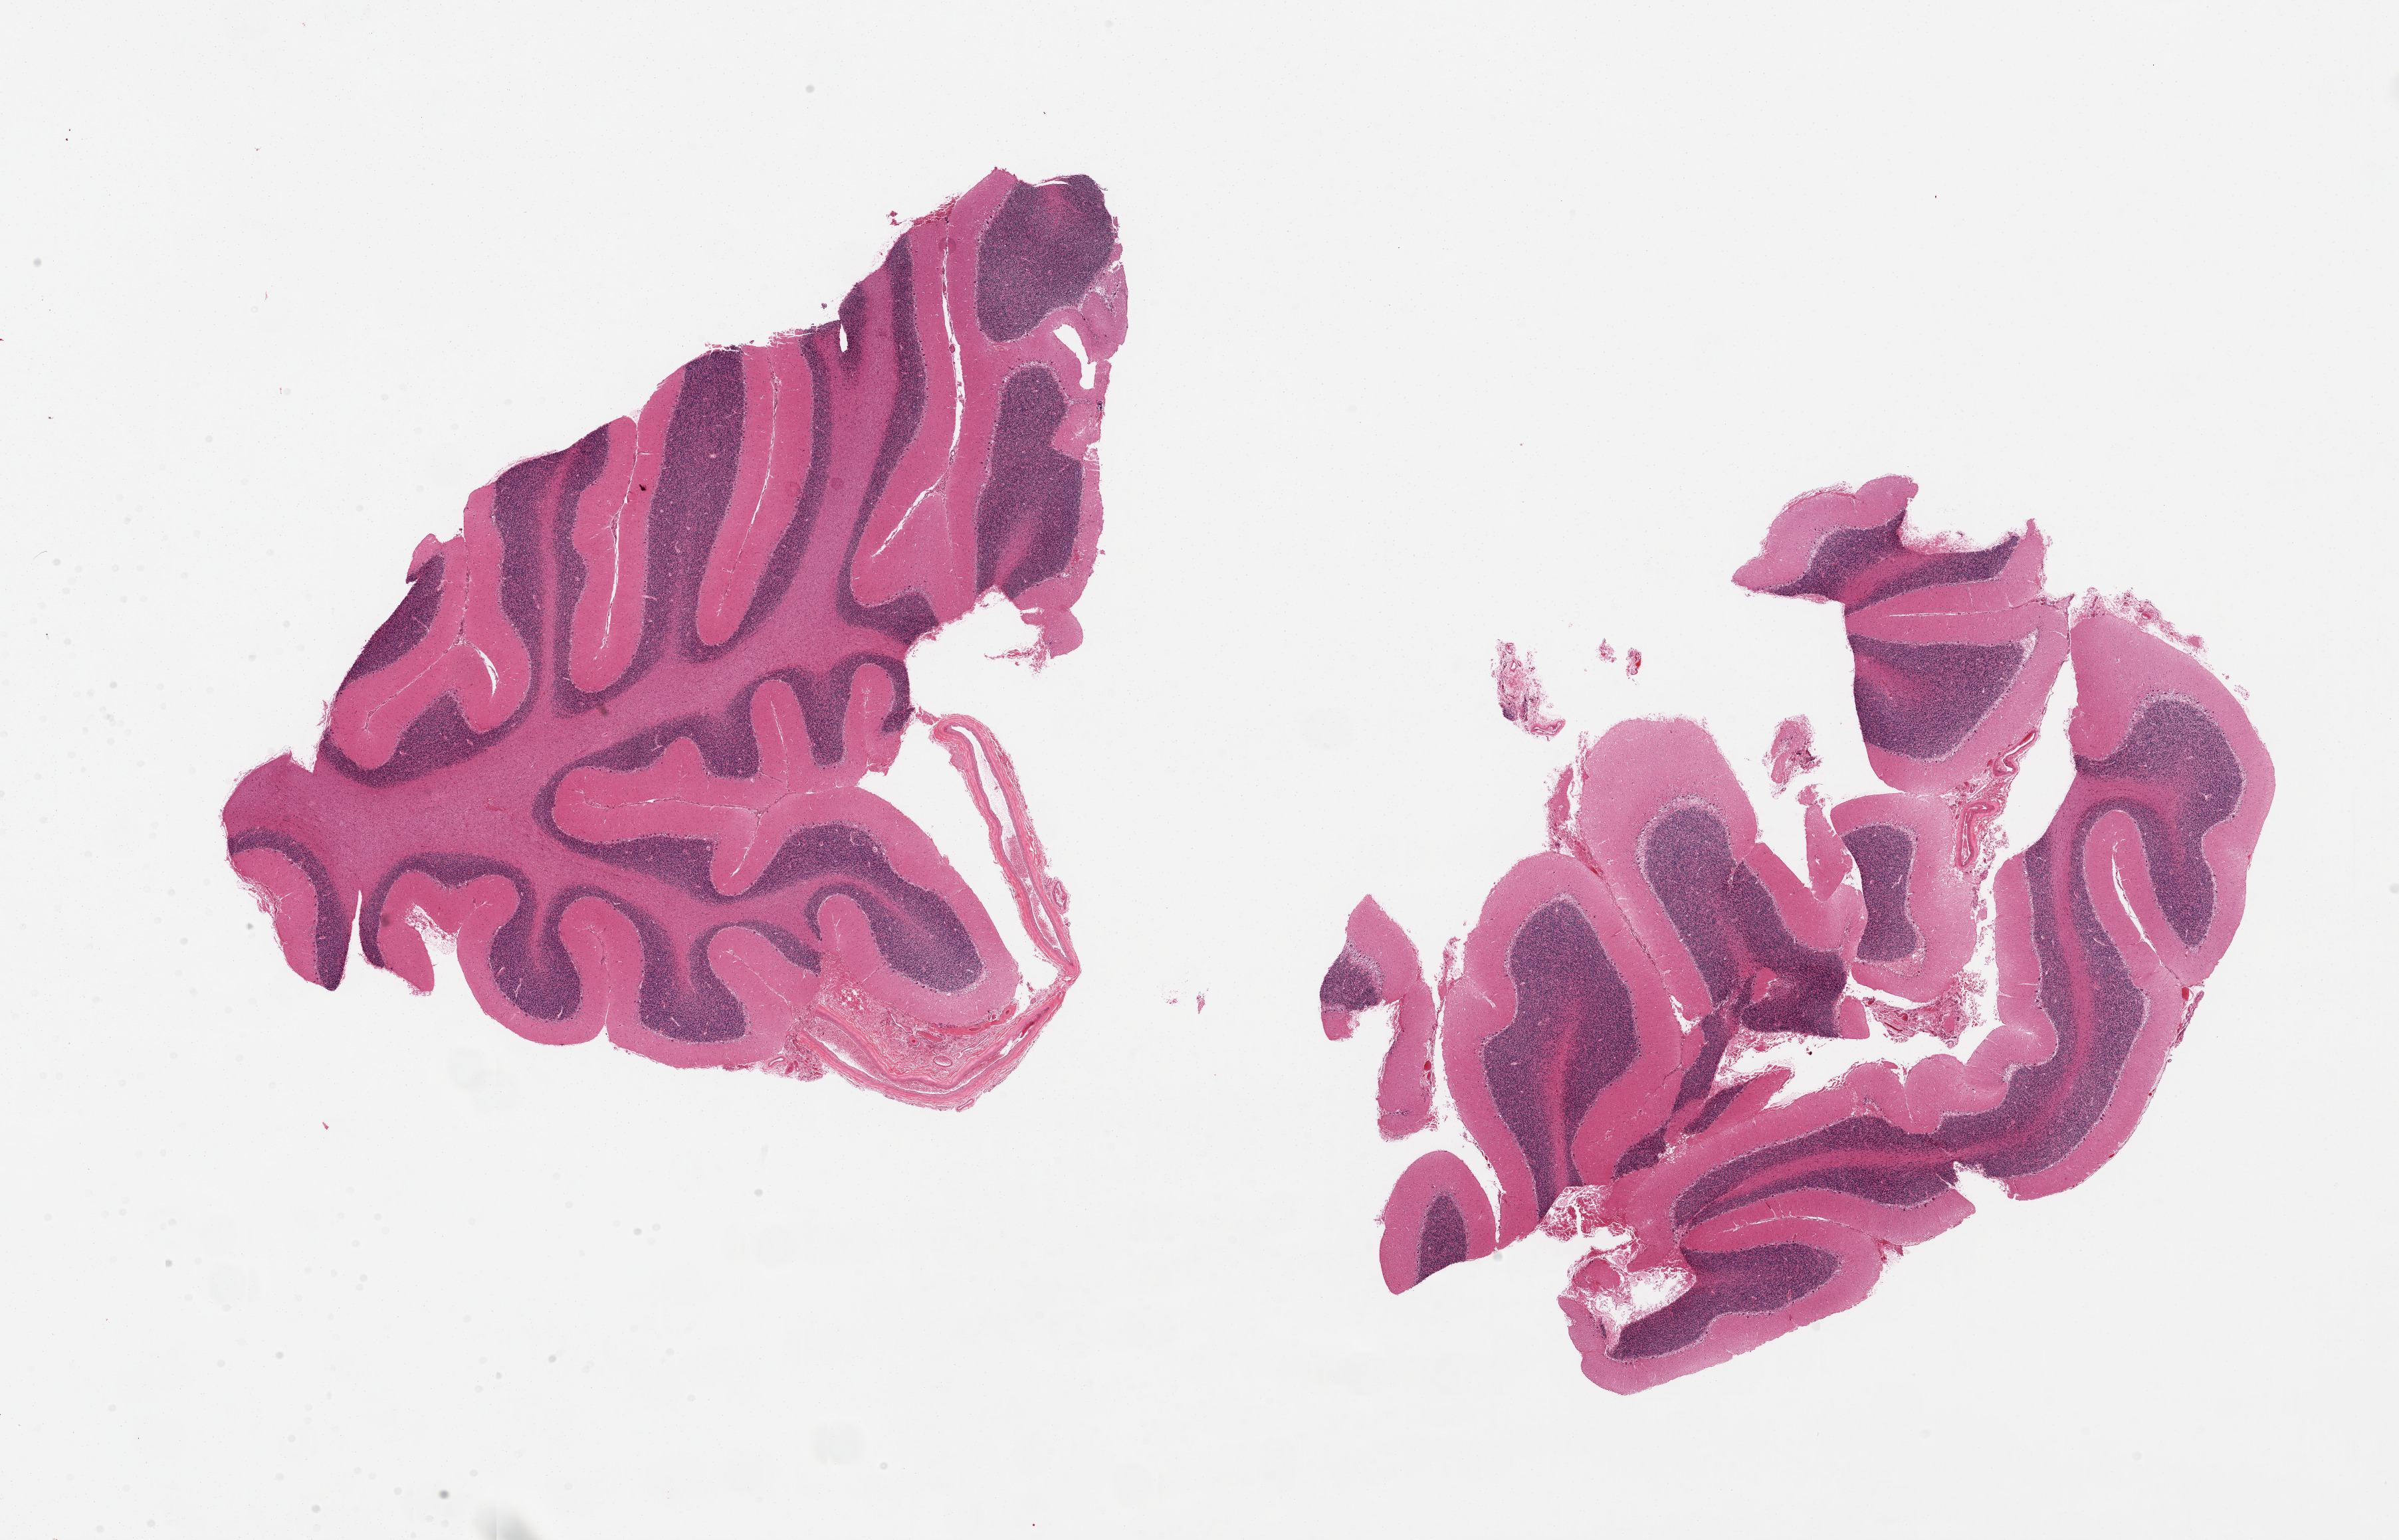
Whole-slide image, hematoxylin and eosin (H&E) stain — low-resolution overview of the scanned area, about 28.5 x 18.3 mm (acquisition: 20x scan). PAXgene-fixed paraffin-embedded (PFPE) section. Sampled site (target tissue): cerebellum. Tissue donor sample. Donor: male.
Pathologist's review note for this sample: 2 pieces, Purkinje cells present.